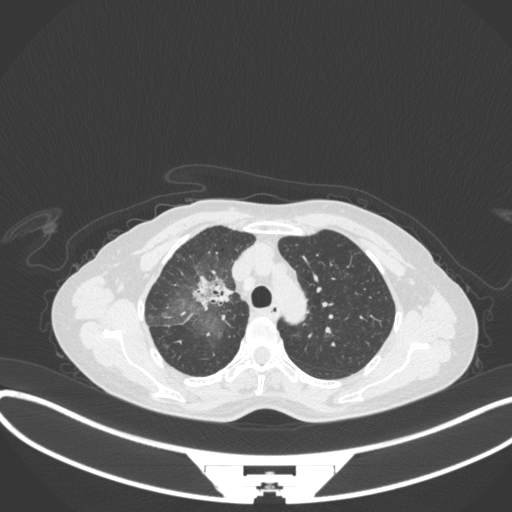
Chest CT, one axial slice. Slice 237 of 311 in the series (ordered by position). Lung window (W 1500 / L -600 HU). 512 × 512 image matrix, field of view 400 × 400 mm. Patient: female, 59 years. Case-level facts recorded for this patient, not image findings: clinical TNM (as recorded): T3 N0 M0; histopathological grade: G1.
Annotated regions visible in this slice (rectangle marked by the reading radiologist):
- lung tumour (recorded histology: adenocarcinoma): bounding box [x1, y1, x2, y2] px = [189, 271, 234, 312]